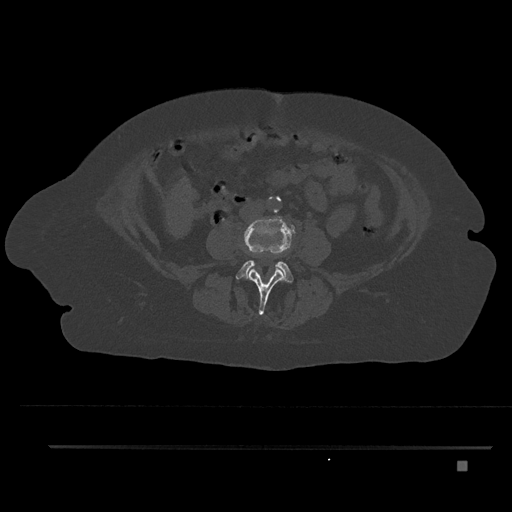
CT including the spine, one axial slice; reconstruction kernel Br40s/3; 120 kVp; bone window (W 1800 / L 400 HU); 0.5 mm slice thickness; 512 × 512 image matrix. Female patient, age 76 years. Case-level facts recorded for this patient, not image findings: primary cancer: lung; vertebrae with lytic lesions (as recorded): T11, L3.
Annotated regions visible in this slice (semi-automatic segmentation, software-assisted and operator-edited):
- L3 vertebra: bounding box <249,266,285,315> (left, top, right, bottom; pixels)
- L4 vertebra: <236,217,294,283>